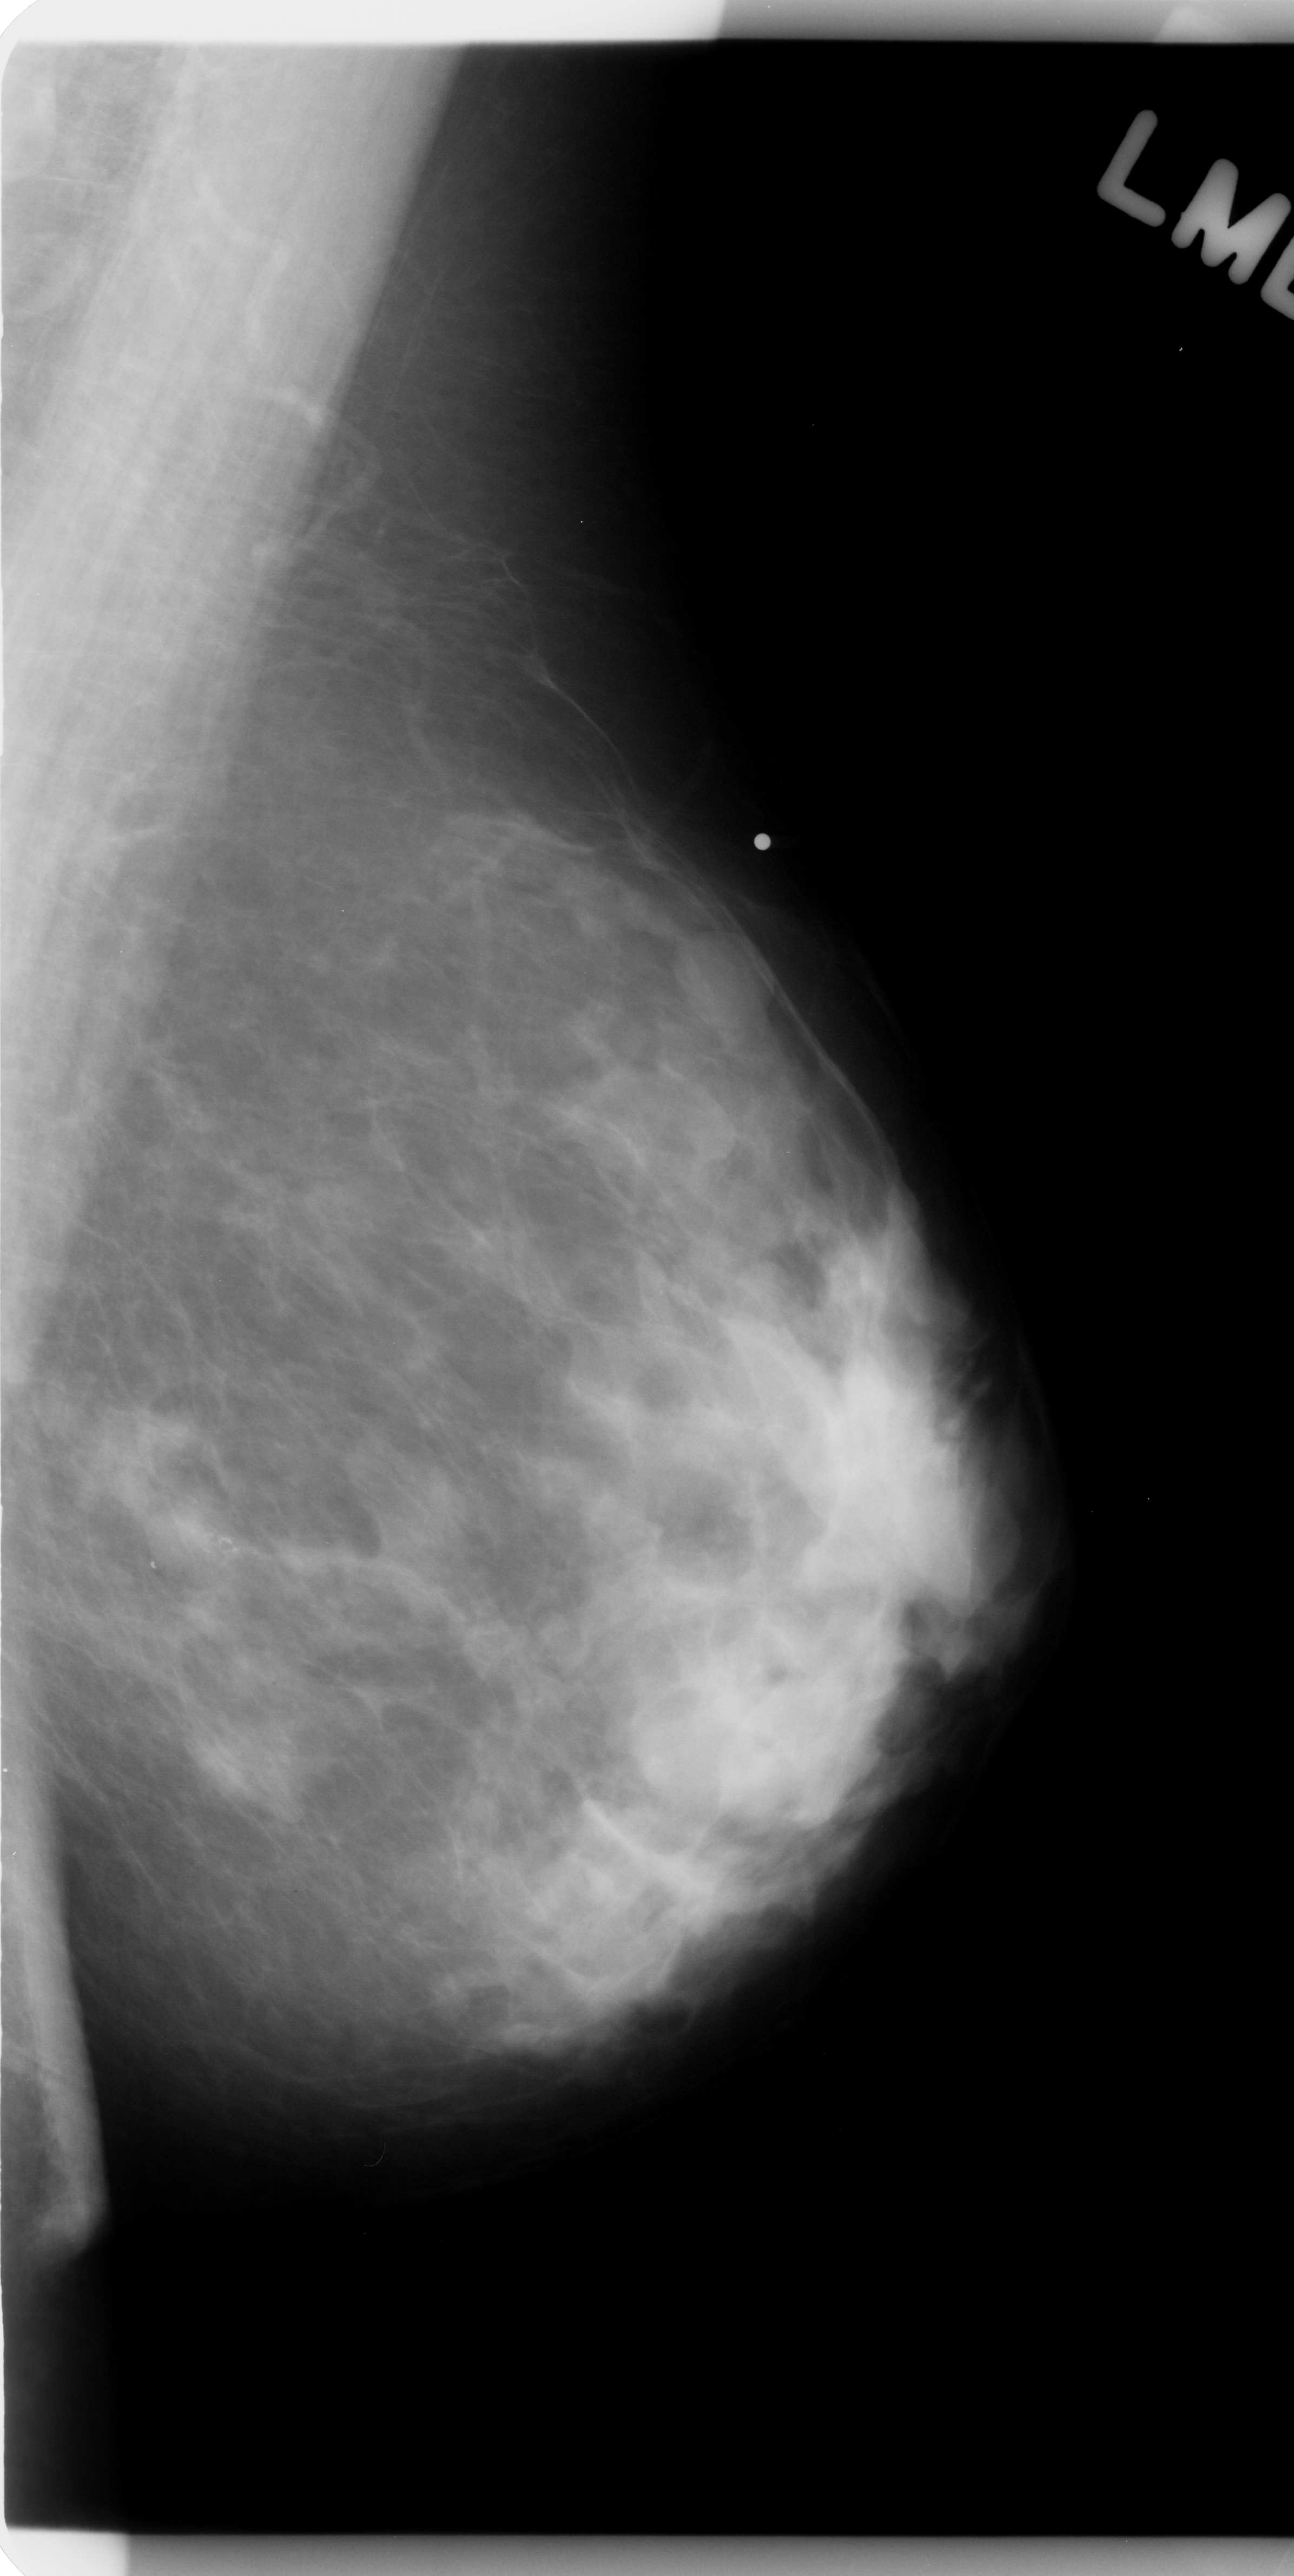
Scanned film-screen mammogram; left breast; MLO view; BI-RADS breast density category 3 (scale 1–4).
Finding: calcifications, morphology amorphous, distribution clustered; BI-RADS assessment category 4; pathology result (as recorded, not read from the image): benign.